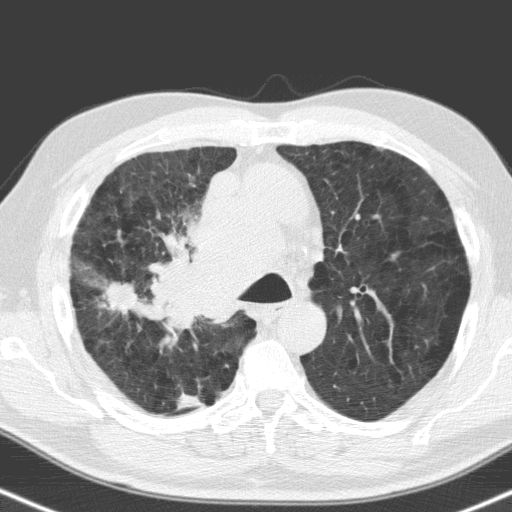
Low-dose screening chest CT, one axial slice; lung window (W 1500 / L -600 HU); 3.2 mm slice thickness; 512 × 512 image matrix, field of view 324 × 324 mm.
Structures marked on this image (manually delineated by an expert):
- lesion 1 (tumor, hilum of right lung): bounding box <155,170,267,327> (left, top, right, bottom; pixels)
- lesion 2 (tumor, upper lobe of right lung): <106,282,137,311>